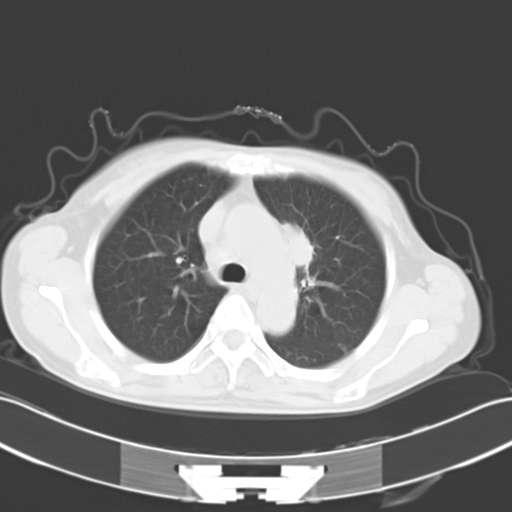
Chest CT, one axial slice. Position 20 of 27 along the scan axis. 120 kVp. Lung window (W 1500 / L -600 HU). 10 mm slice thickness. 512 × 512 image matrix, field of view 353 × 353 mm. Female patient, age 50 years. Case-level facts recorded for this patient, not image findings: clinical TNM (as recorded): T2a N1 M1c.
Structures marked on this image (bounding box drawn by a radiologist):
- lung tumour (recorded histology: adenocarcinoma): bounding box <281,222,323,275> (left, top, right, bottom; pixels)